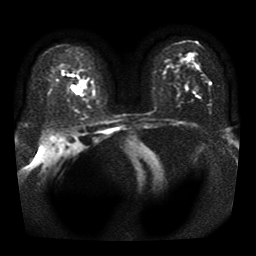
Breast MRI, one axial slice; diffusion-weighted series; image 2 of 4 stored at this slice position (different b-values; order by instance number); 1.5 T; 5 mm slice thickness; 256 × 256 image matrix, field of view 330 × 330 mm. Female patient.
Structures marked on this image (outlined manually by an expert reader):
- tumour on diffusion-weighted imaging: bounding box [x1, y1, x2, y2] px = [70, 84, 82, 95]